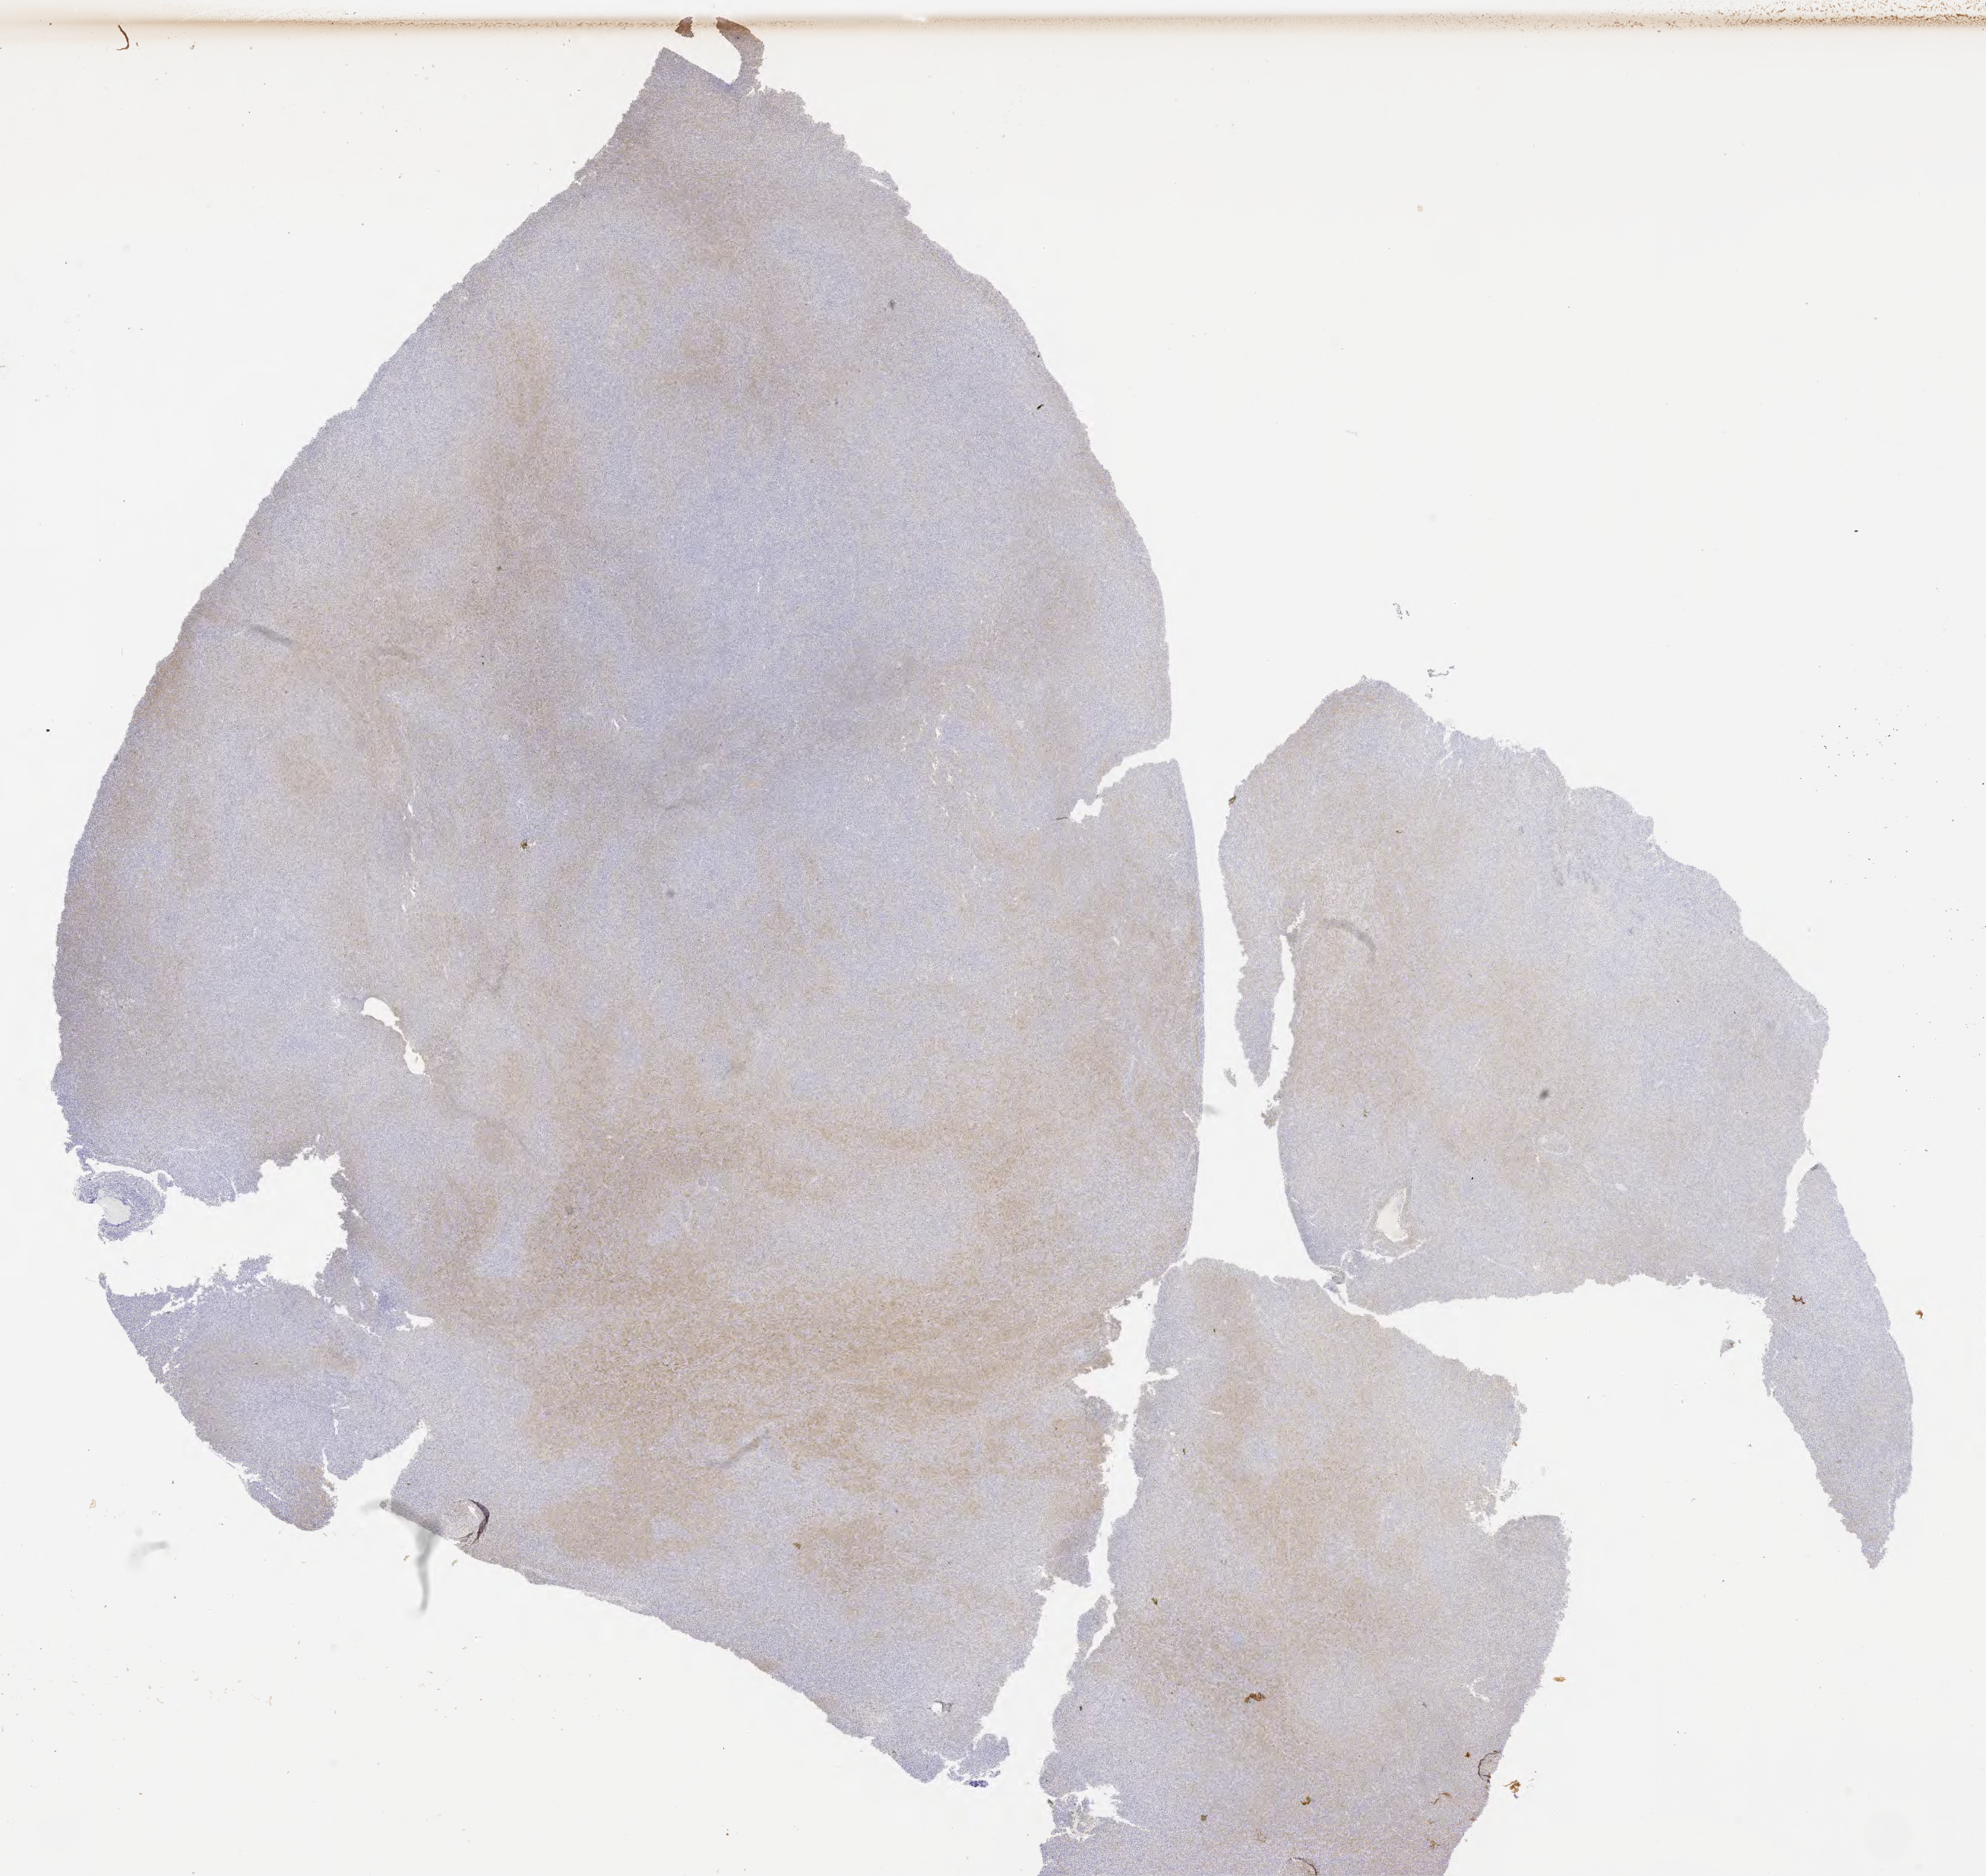
Immunohistochemistry (IHC) whole-slide image stained for CD10, shown as a low-resolution overview of the whole scanned area (about 21.1 x 20.0 mm), specimen: tumor tissue, anatomic site: liver. Patient female; aged 46.
Histologic diagnosis: Diffuse large B-cell lymphoma, NOS.